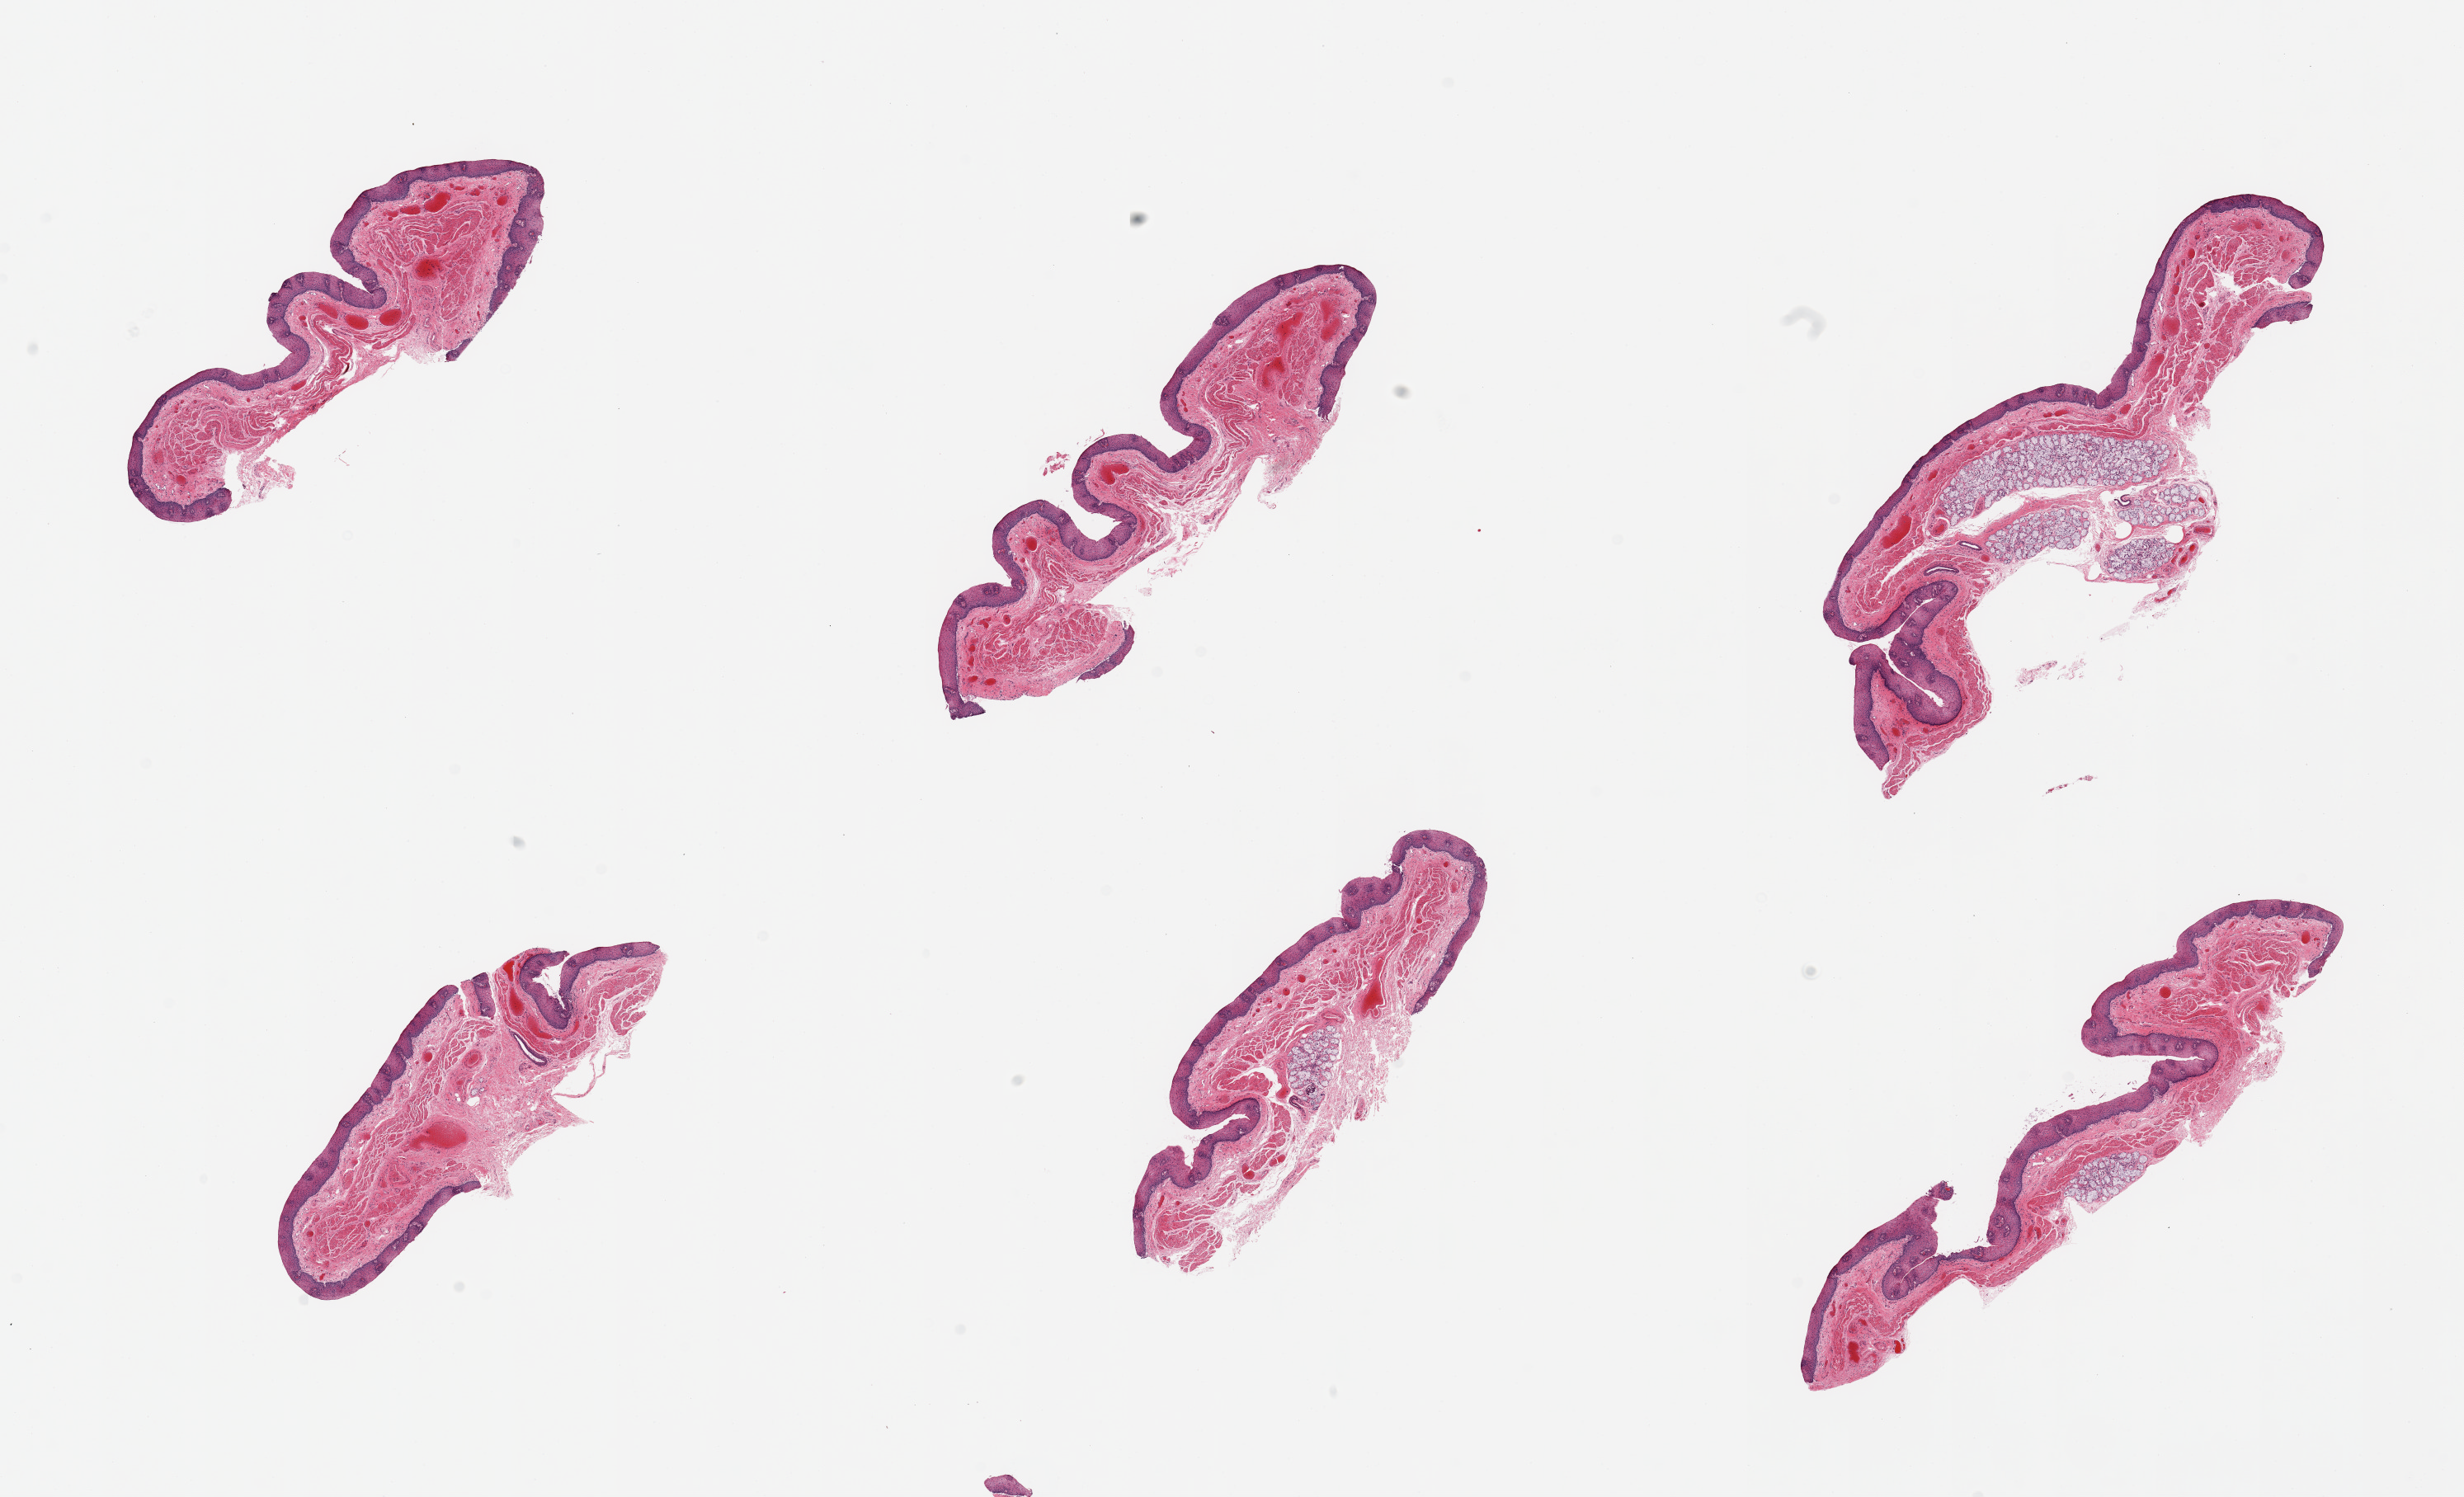
Whole-slide image, haematoxylin and eosin stain, shown as a low-resolution overview of the whole scanned area (about 23.6 x 14.4 mm, acquisition: 20x scan). PAXgene-fixed, paraffin-embedded tissue. Target tissue: esophageal mucous membrane. Donor tissue sample. Donor: male.
Reviewer comment on this tissue sample: 6 pieces; includes several clusters of submucosal glands.